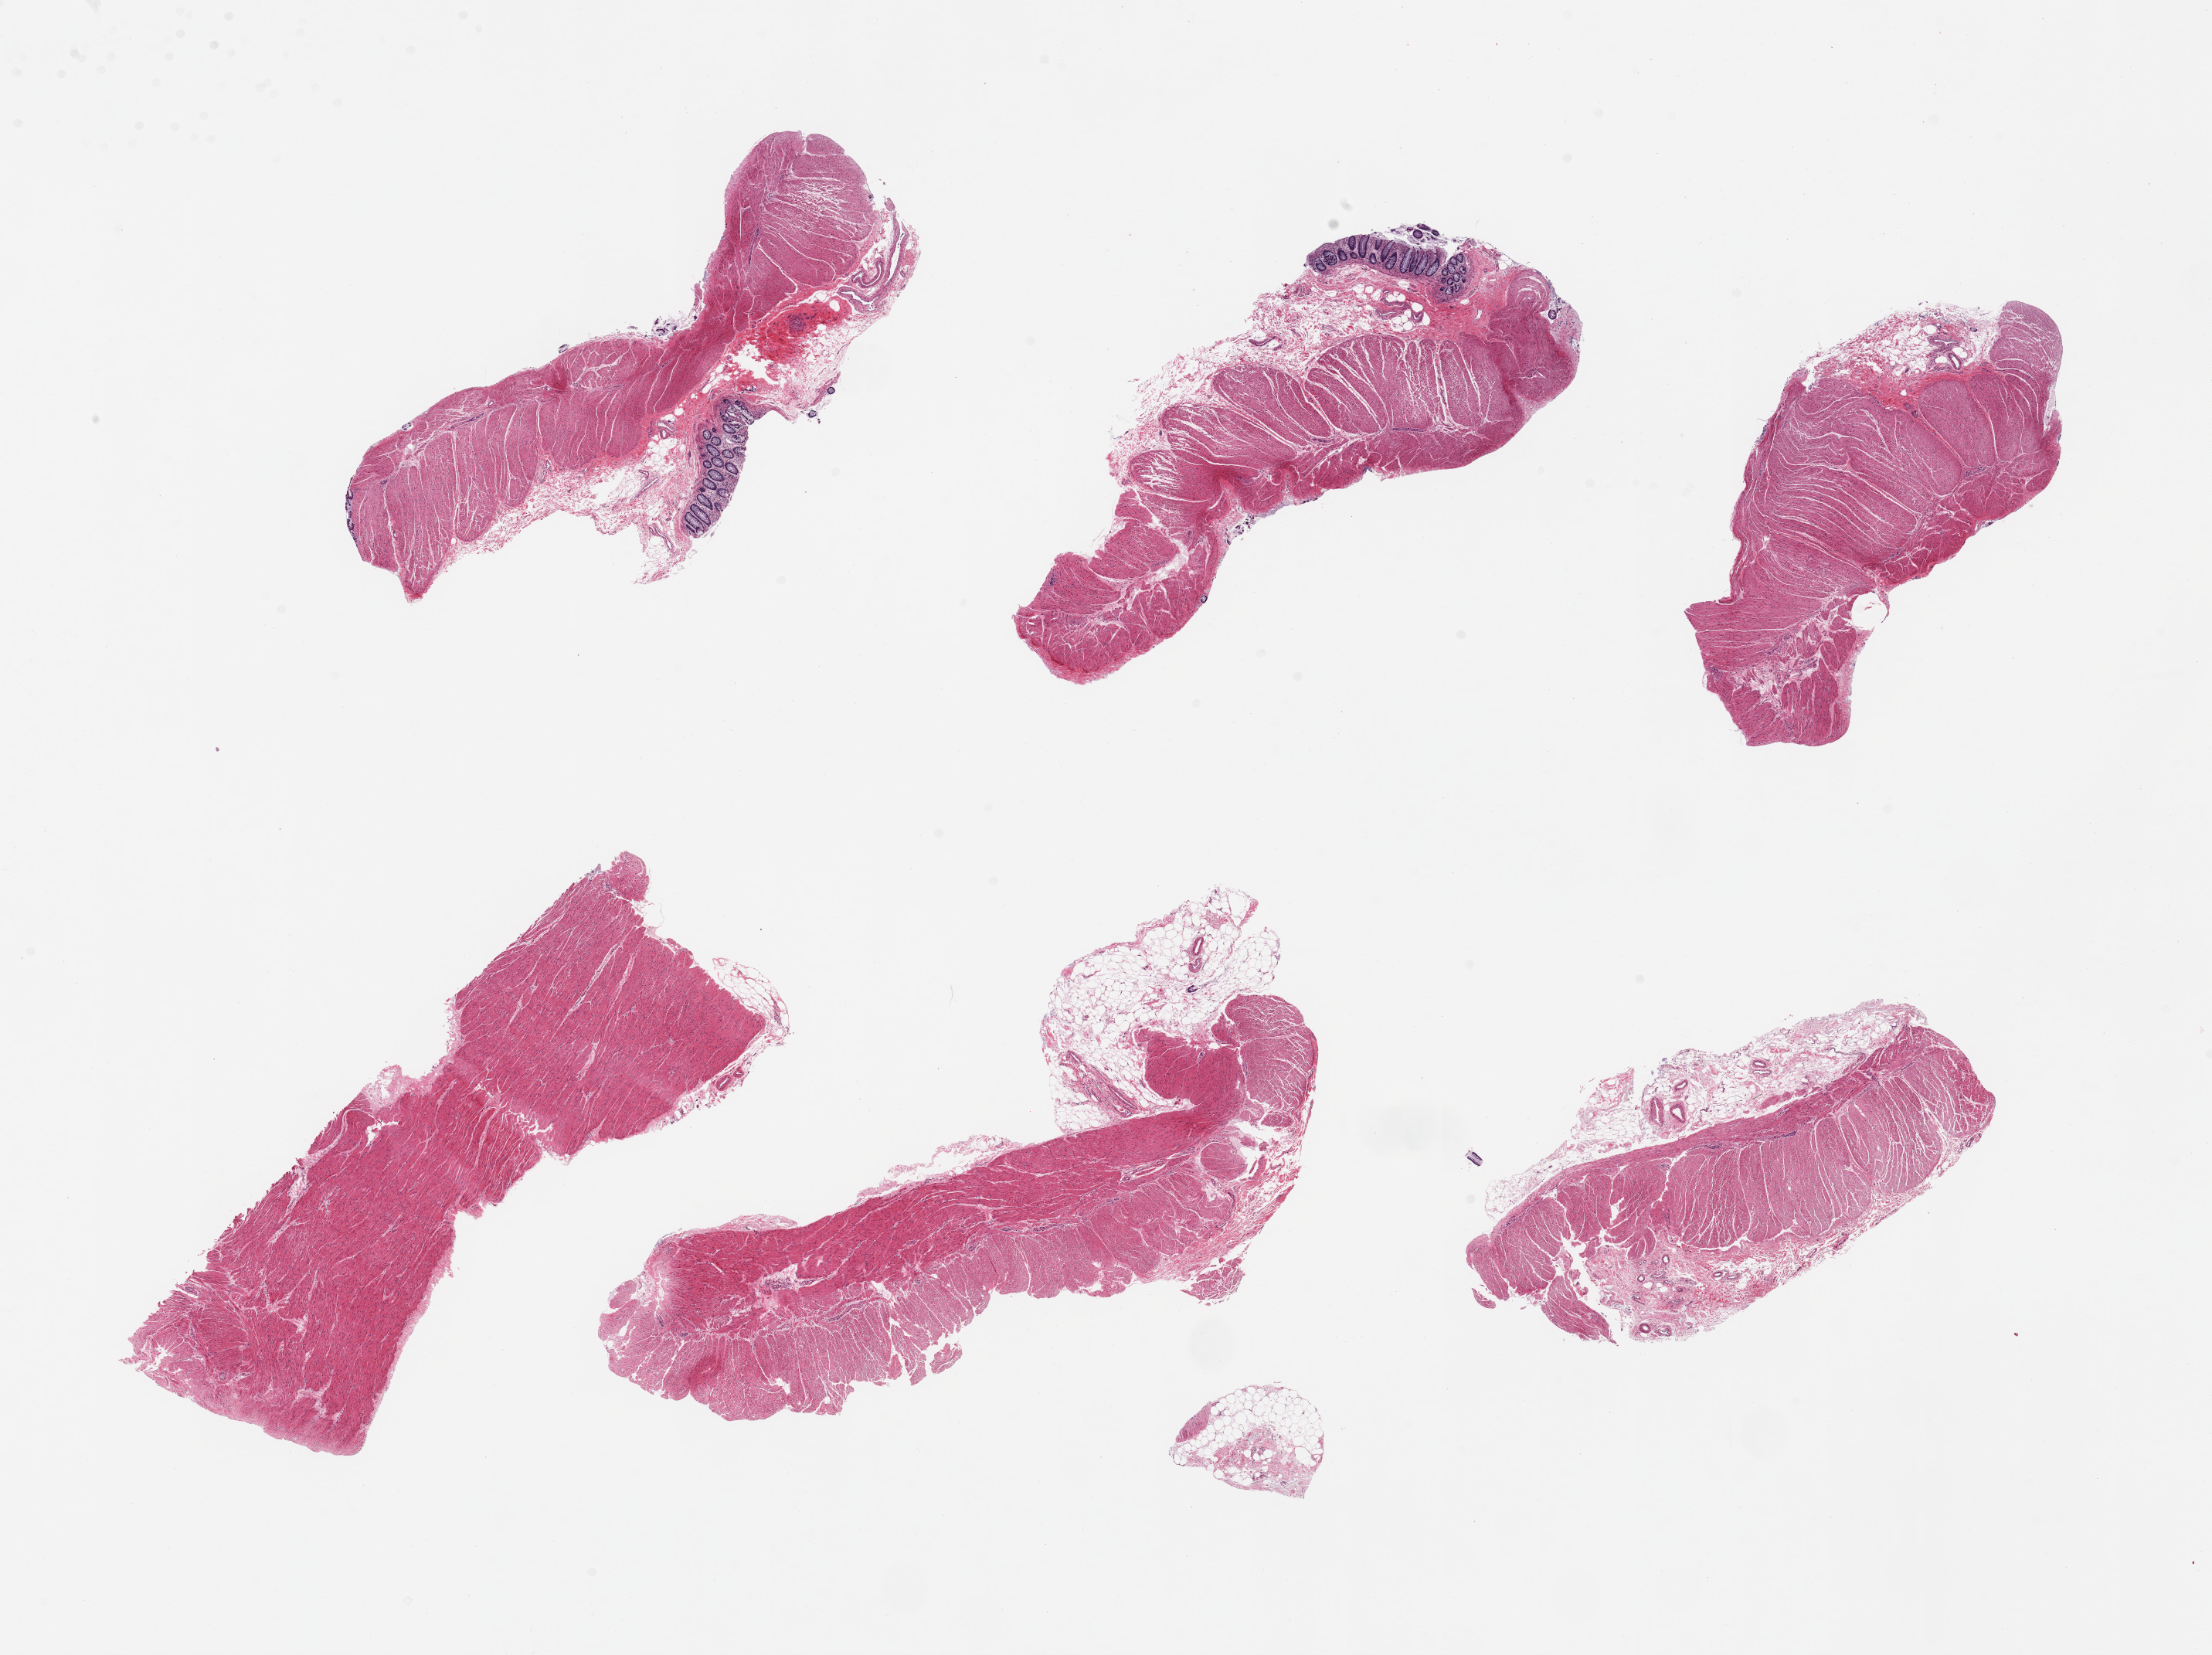
Hematoxylin and eosin (H&E) whole-slide image, whole scanned area (about 22.6 x 16.9 mm) shown as a low-resolution overview. PAXgene-fixed paraffin-embedded (PFPE) section. Target tissue: sigmoid colon. Tissue donor sample. Female donor.
Pathologist's review note for this sample: 6 pieces; predominantly muscularis with some attached fat and residual mucosa.